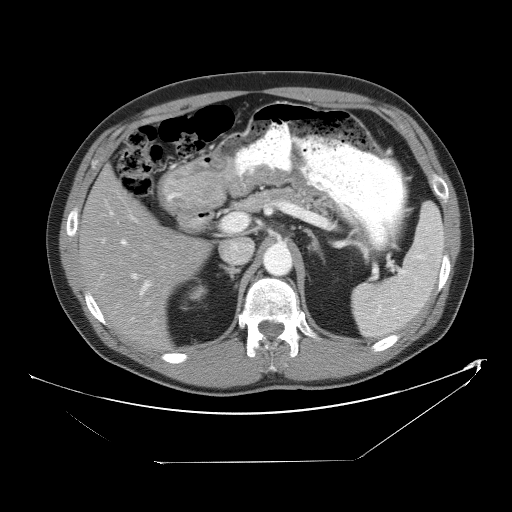
Contrast-enhanced abdominal CT, one axial slice; slice 31 of 53 in the series (ordered by position); reconstruction kernel STANDARD; 120 kVp; intravenous contrast given; soft-tissue window (W 400 / L 40 HU); 5 mm slice thickness; 512 × 512 image matrix, field of view 438 × 438 mm. Male patient, age 59 years. From the clinical record (not read from this slice): diagnosis: colorectal cancer liver metastases, imaged before liver resection; multiple liver metastases: yes; largest metastasis: 8.5 cm; chemotherapy before resection: yes.
Outlined on this slice (expert manual segmentation):
- hepatic veins: bounding box <102,199,150,306> (left, top, right, bottom; pixels)
- liver: <80,171,208,348>
- planned liver remnant (the part of the liver to remain after resection): <80,171,209,349>
- portal vein (with intrahepatic branches): <121,214,247,295>